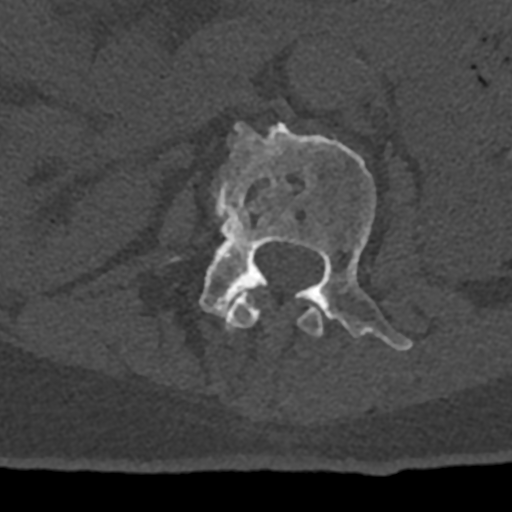
CT including the spine, one axial slice; reconstruction kernel Br40s/3; 120 kVp; bone window (W 1800 / L 400 HU); 512 × 512 image matrix, field of view 160 × 160 mm. Patient: male, 74 years. Case-level facts recorded for this patient, not image findings: primary cancer: renal; vertebrae with lytic lesions (as recorded): T10, L1, L2, L3, L4, L5.
Structures marked on this image (semi-automatically segmented with operator editing):
- L1 vertebra: bounding box [x1, y1, x2, y2] px = [225, 288, 323, 337]
- L2 vertebra: [199, 122, 413, 351]